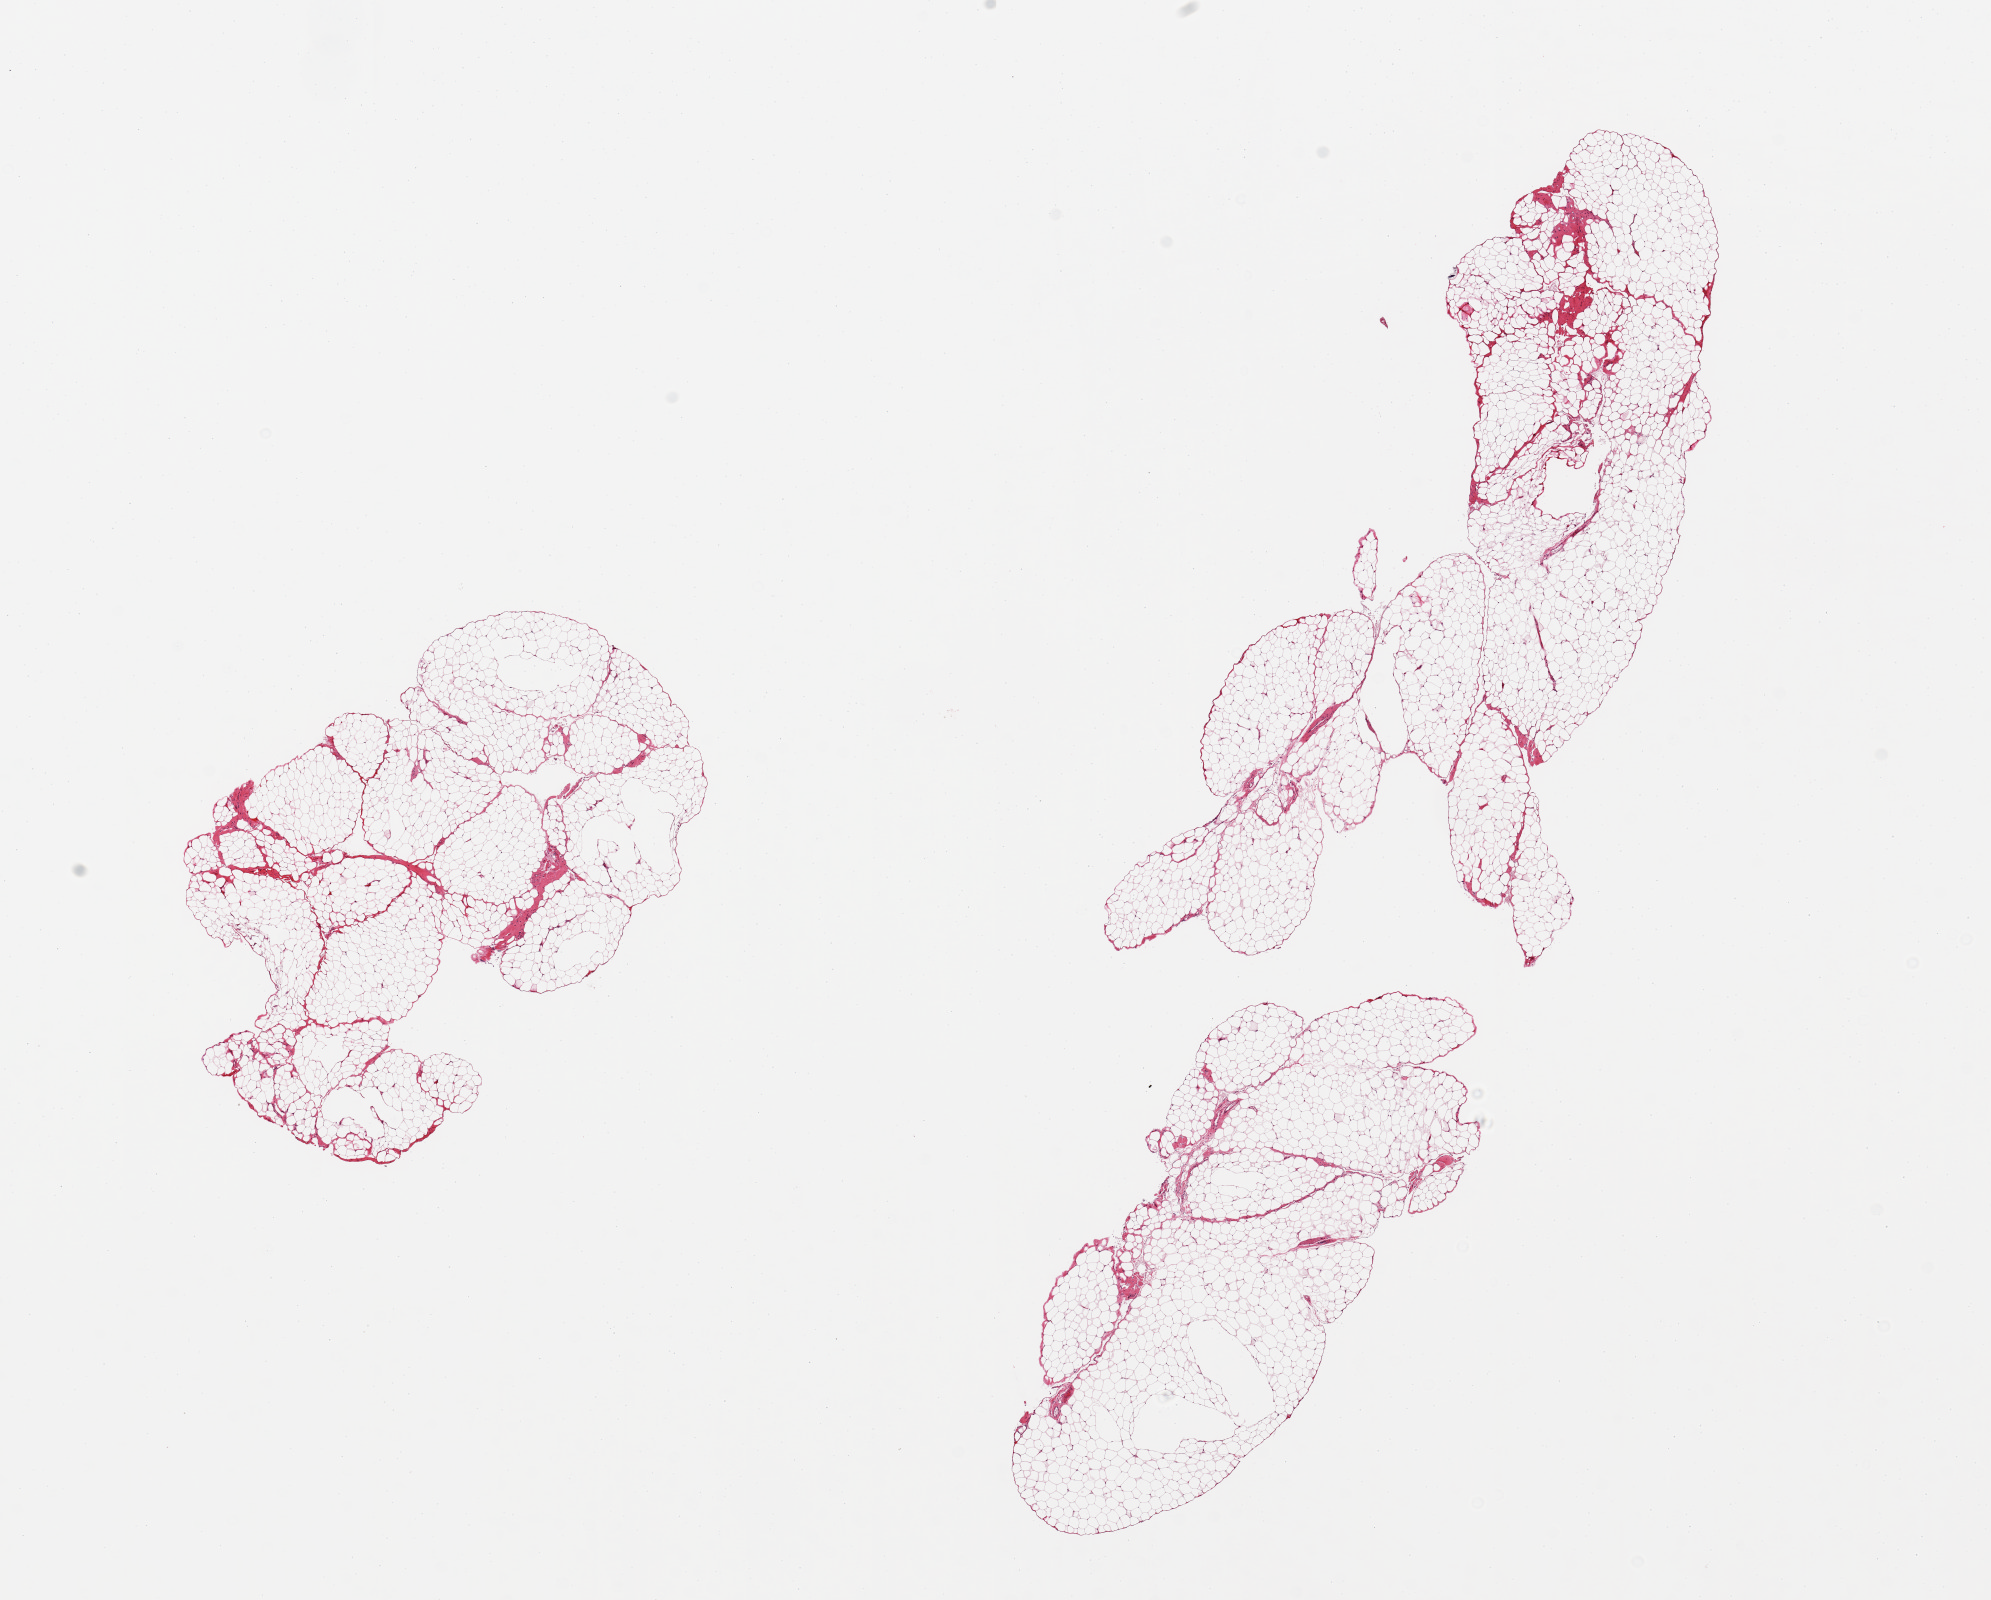
H&E whole-slide image, brightfield, a low-resolution overview of the entire scanned area, about 15.8 x 12.7 mm (acquisition: 20x scan); PAXgene-fixed, paraffin-embedded tissue; target tissue: omentum; tissue donor sample. Male donor.
Reviewer comment on this tissue sample: 3 pieces.